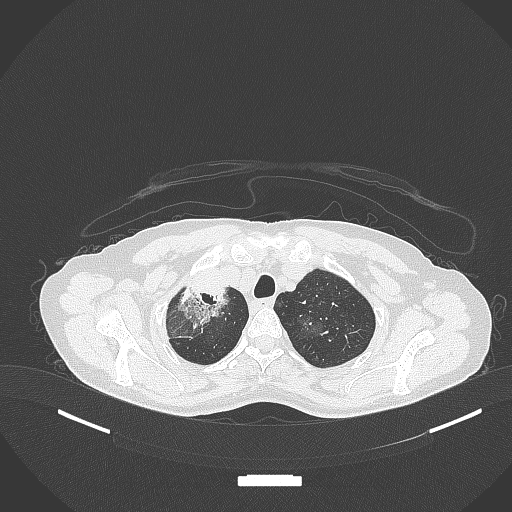
Chest CT, one axial slice; slice 279 of 284 in the series (ordered by position); lung window (W 1500 / L -600 HU); 1 mm slice thickness; 512 × 512 image matrix, field of view 400 × 400 mm. Female patient, age 59 years. Case-level facts recorded for this patient, not image findings: clinical TNM (as recorded): T3 N0 M0.
Structures marked on this image (bounding box drawn by a radiologist):
- lung tumour (recorded histology: adenocarcinoma): bounding box [x1, y1, x2, y2] px = [176, 279, 227, 324]